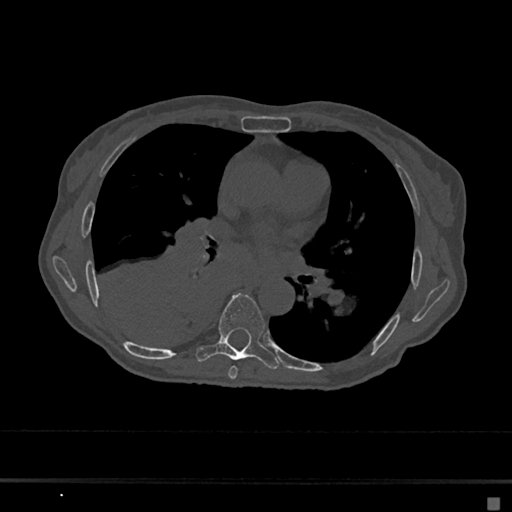
CT including the spine, one axial slice; position 379 of 797 along the scan axis; 120 kVp; bone window (W 1800 / L 400 HU); 0.5 mm slice thickness; 512 × 512 image matrix. Patient: female, 68 years. From the clinical record (not read from this slice): primary cancer: renal.
Structures marked on this image (semi-automatically segmented with operator editing):
- T6 vertebra: bounding box <228,366,238,379> (left, top, right, bottom; pixels)
- T7 vertebra: <196,293,280,370>